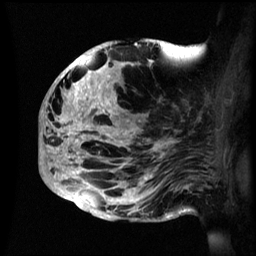
Breast MRI (dynamic contrast-enhanced), one sagittal slice; slice 28 of 60 in the series (ordered by position); dynamic contrast-enhanced series, image 2 of 3 at this slice position (ordered by acquisition); 1.5 T; TE 4.2 ms, TR 8.4 ms; 2.4 mm slice thickness; 256 × 256 image matrix, field of view 230 × 230 mm. Female patient, age 48 years.
Structures marked on this image (semi-automatically segmented with operator editing):
- analysis volume of interest (the breast-tissue region the enhancement analysis was run in; not a lesion): bounding box (x1, y1, x2, y2) in pixels: (40, 41, 195, 222)
- tumour enhancement mask (voxels above the 70 % enhancement threshold inside the analysis volume of interest): (40, 41, 178, 219)